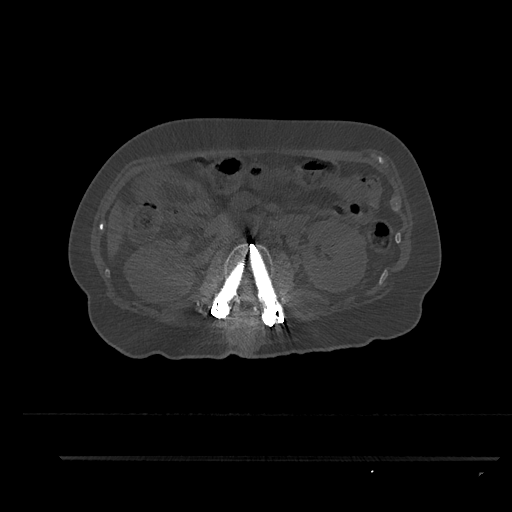
CT including the spine, one axial slice. Position 169 of 797 along the scan axis. Reconstruction kernel Br40s/3. 120 kVp. Bone window (W 1800 / L 400 HU). 0.5 mm slice thickness. 512 × 512 image matrix. Female patient, age 44 years. Case-level facts recorded for this patient, not image findings: primary cancer: renal.
Annotated regions visible in this slice (semi-automatically segmented with operator editing):
- L2 vertebra: bounding box <208,243,284,319> (left, top, right, bottom; pixels)